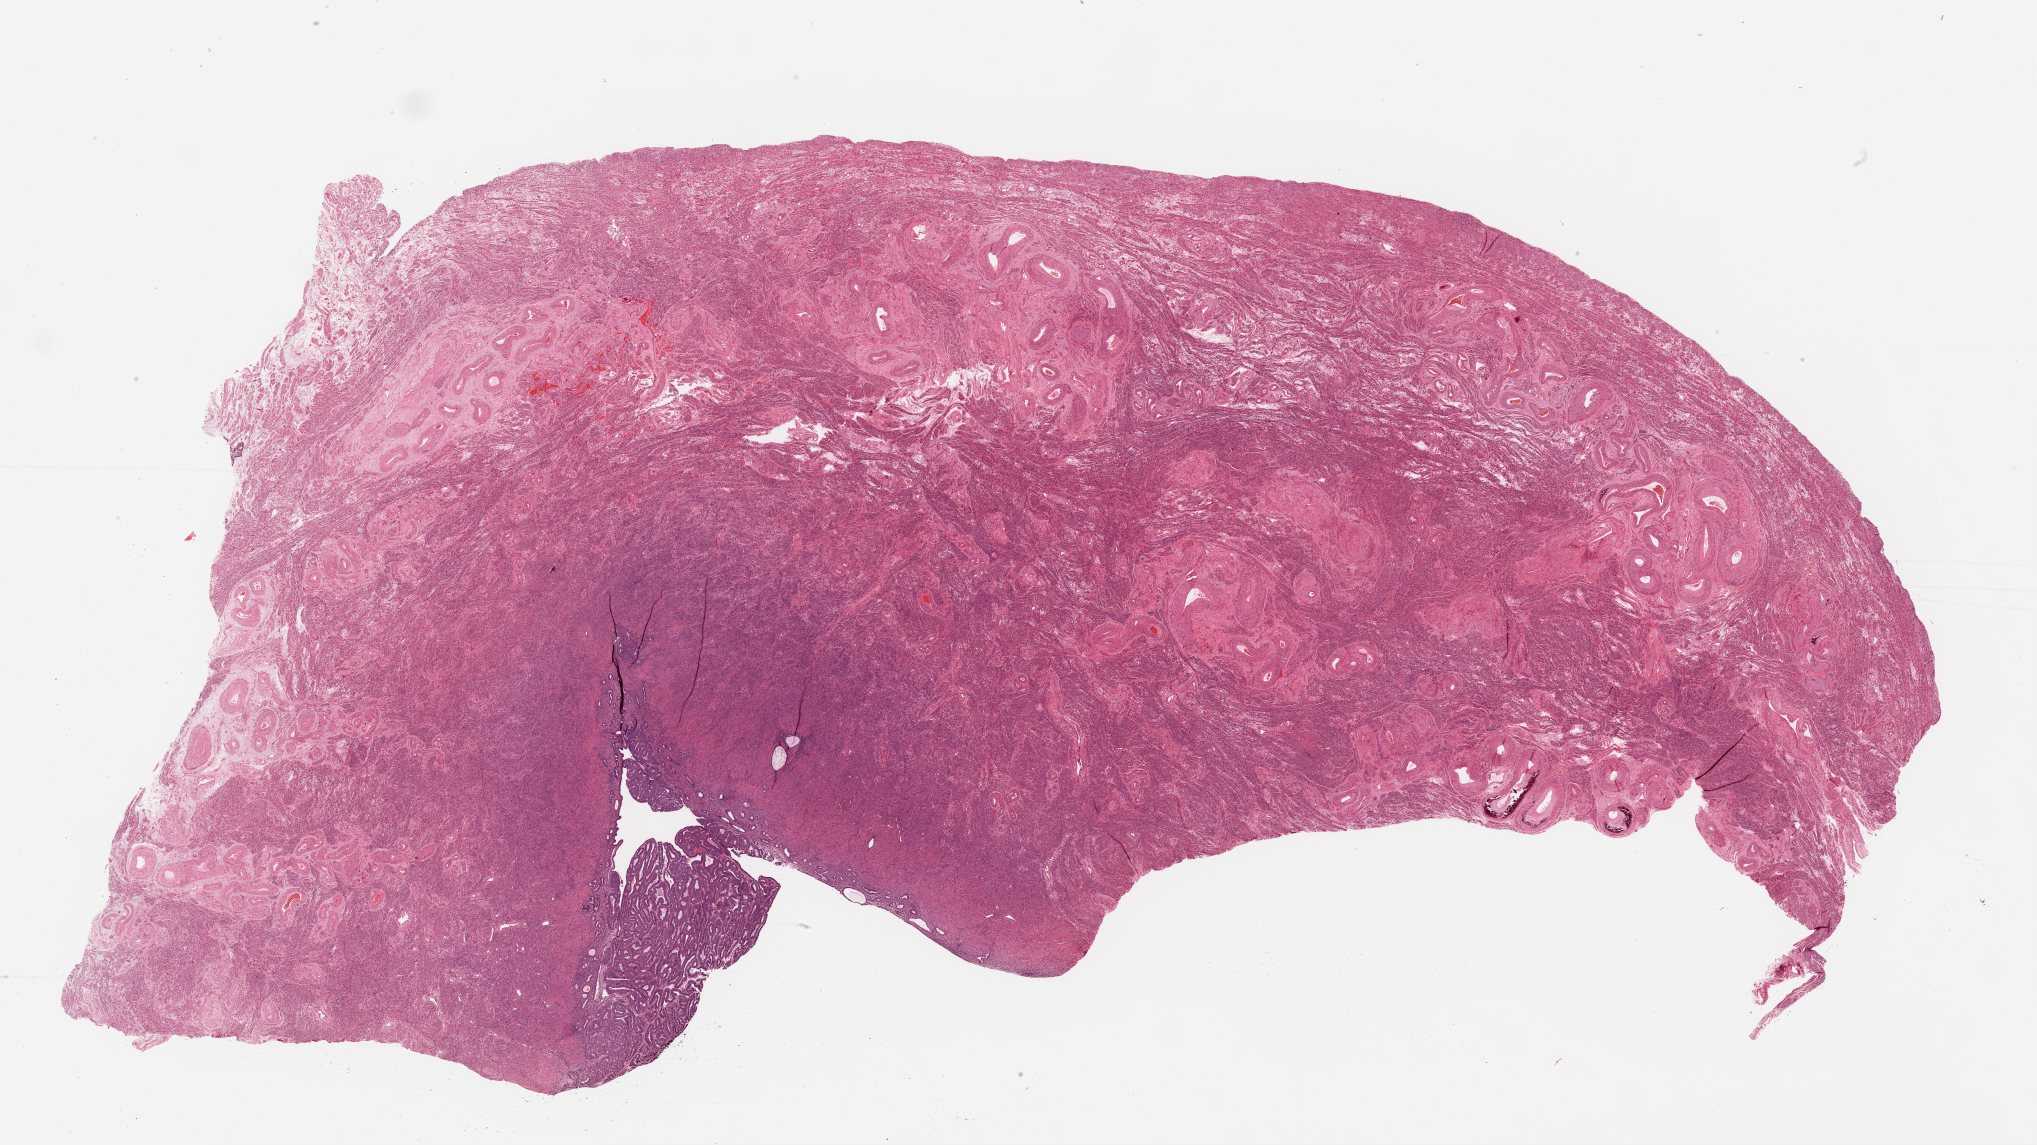
Whole-slide histology image, H&E-stained — whole scanned area (about 32.2 x 18.1 mm) shown as a low-resolution overview, formalin-fixed paraffin-embedded (FFPE) diagnostic section, primary tumour sample from the uterus. Patient: female, age at initial diagnosis 81 years. Histologic grade: G2 (moderately differentiated).
- FIGO stage: IIA
- pathologic diagnosis: Endometrioid adenocarcinoma, NOS (endometrium)